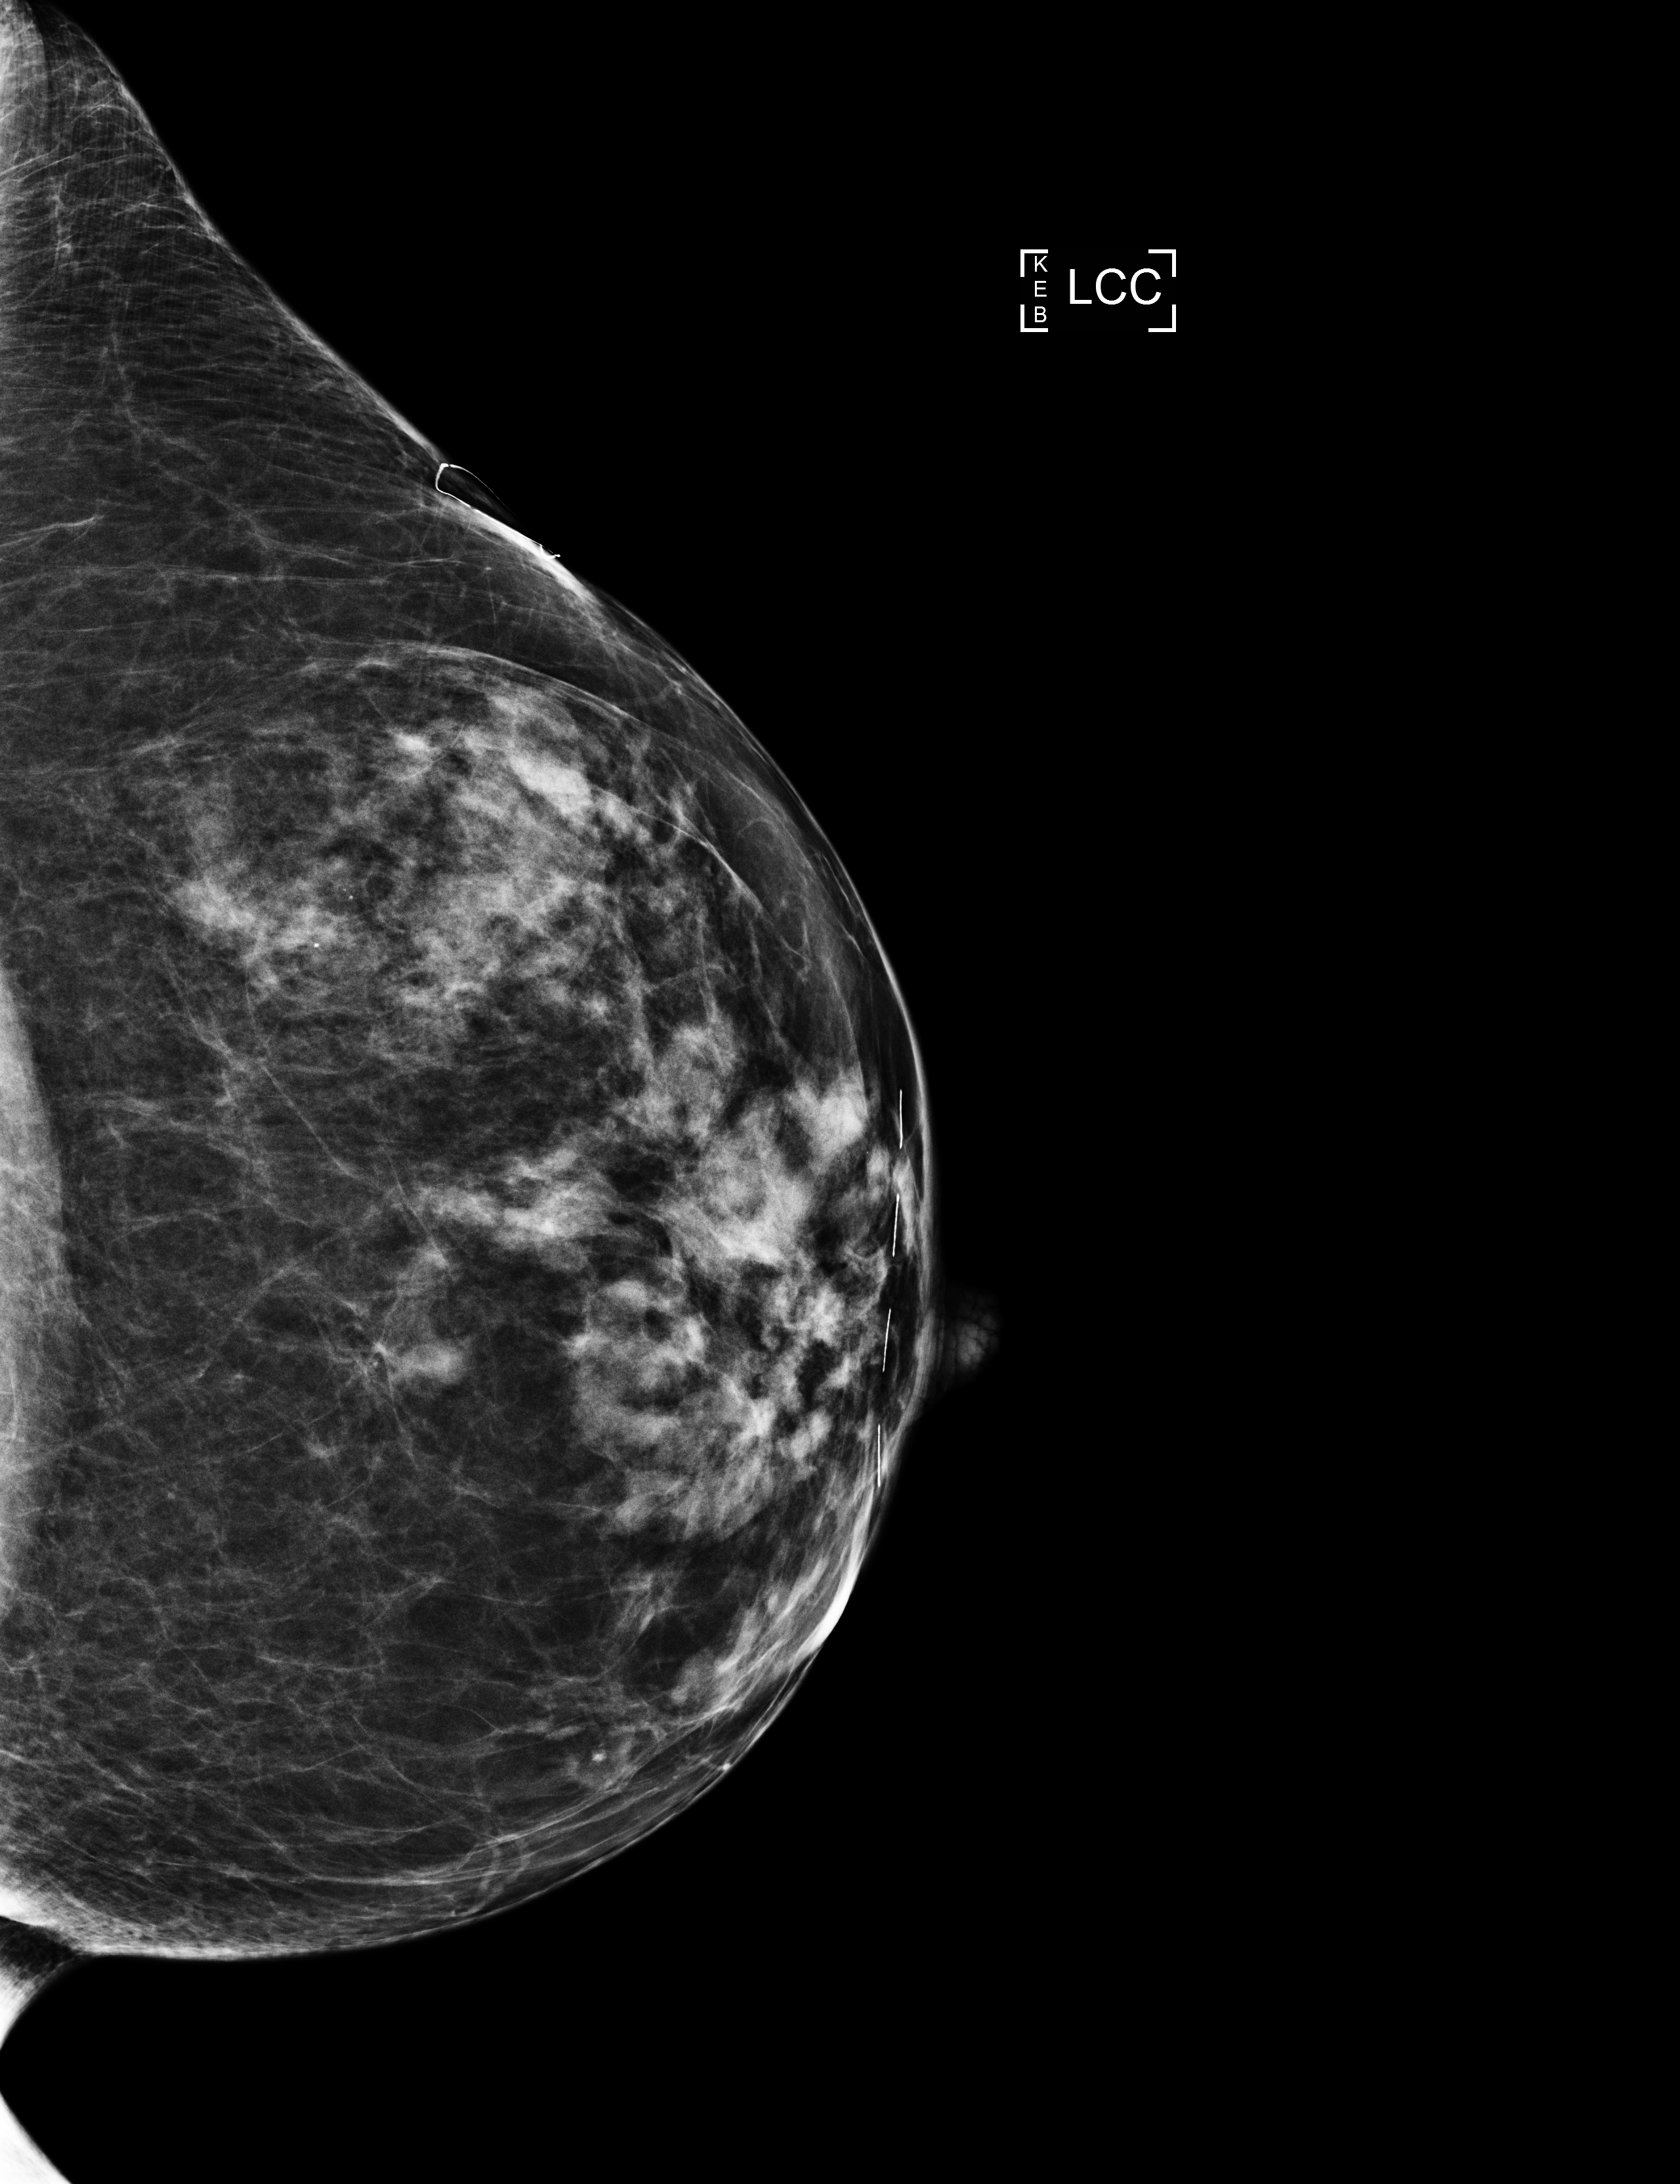
Annual screening mammography examination. Patient: female, 73 years.
Image type: full-field digital mammogram. Breast: left. Projection: CC view.